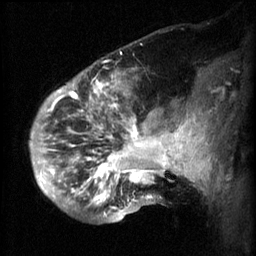
Breast MRI (dynamic contrast-enhanced), one sagittal slice; position 18 of 60 along the scan axis; 3 images stored at this slice position (order not interpretable as contrast timing); 1.5 T; TE 4.2 ms, TR 8.2 ms; 256 × 256 image matrix. Patient: female, 50 years.
Annotated regions visible in this slice (semi-automatically segmented with operator editing):
- analysis volume of interest (the breast-tissue region the enhancement analysis was run in; not a lesion): bounding box (x1, y1, x2, y2) in pixels: (50, 64, 169, 217)
- tumour enhancement mask (voxels above the 70 % enhancement threshold inside the analysis volume of interest): (50, 80, 169, 217)